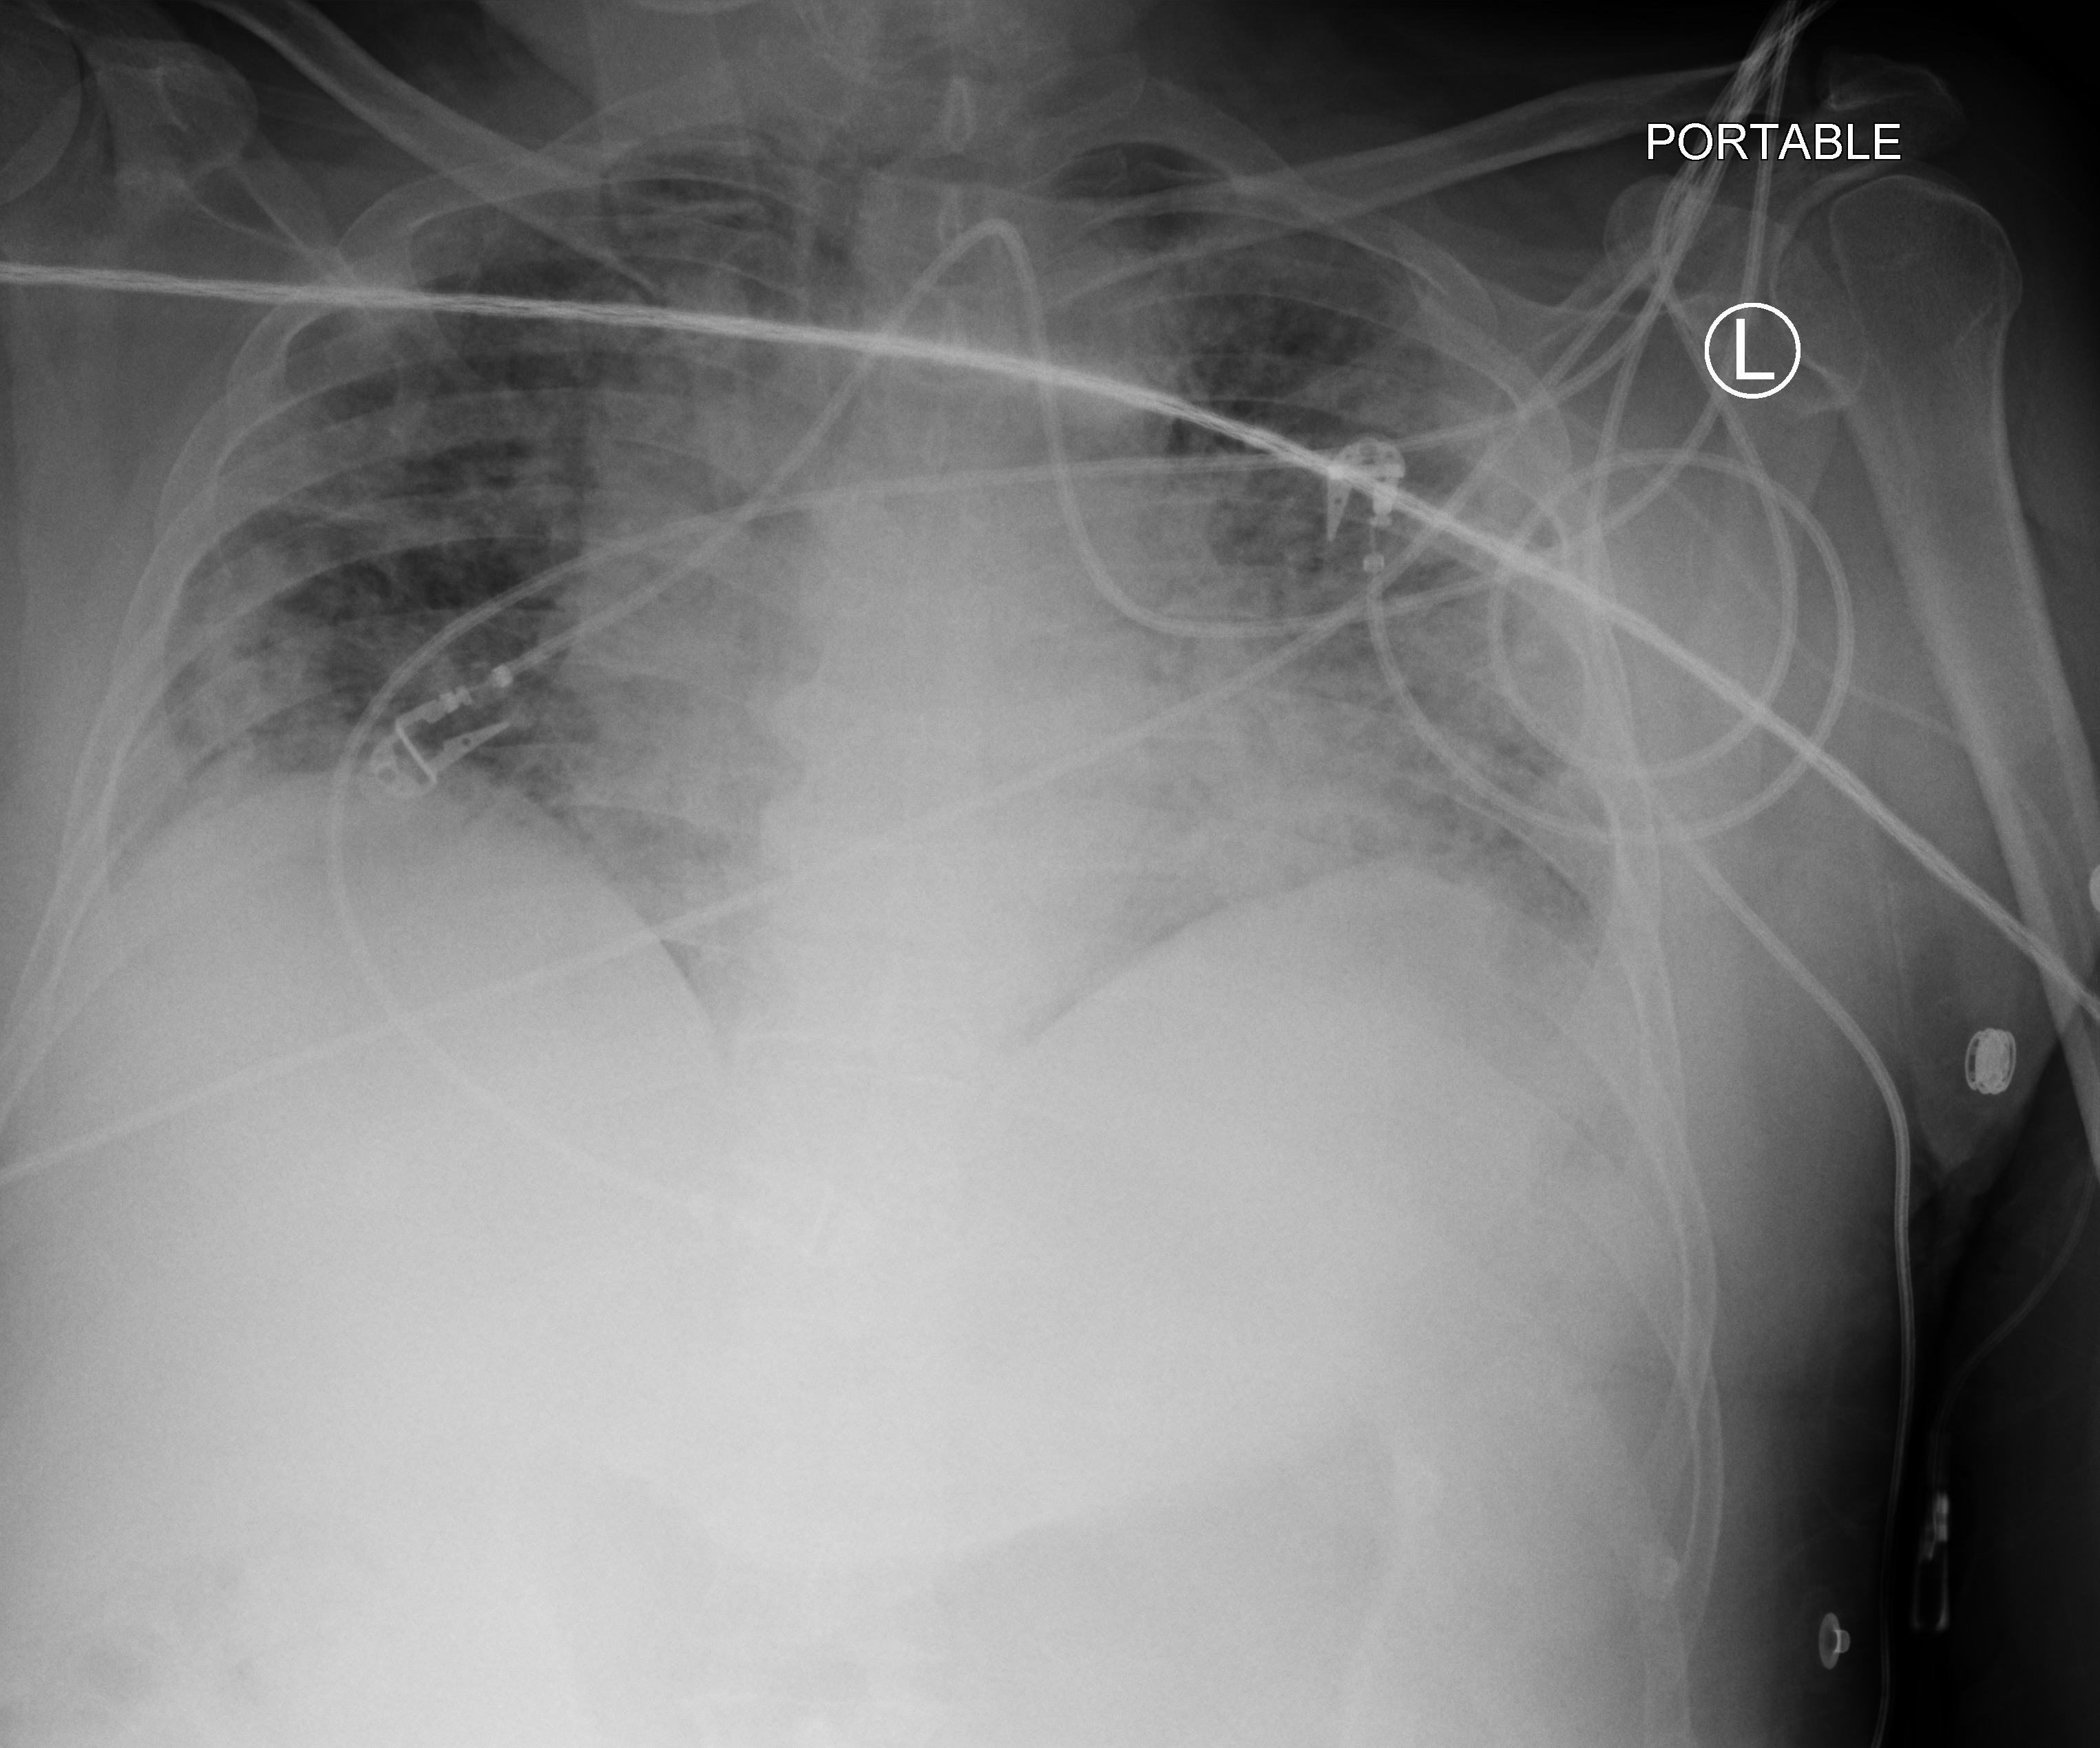
Bedside chest radiograph (computed radiography), anteroposterior (AP) projection. Male patient hospitalised with COVID-19, age 60–74 years.
Hospital-stay facts (about this admission, not read from this image; timing relative to this image not recorded):
- mechanically ventilated during this hospital stay: yes
- admitted to intensive care during this hospital stay: yes